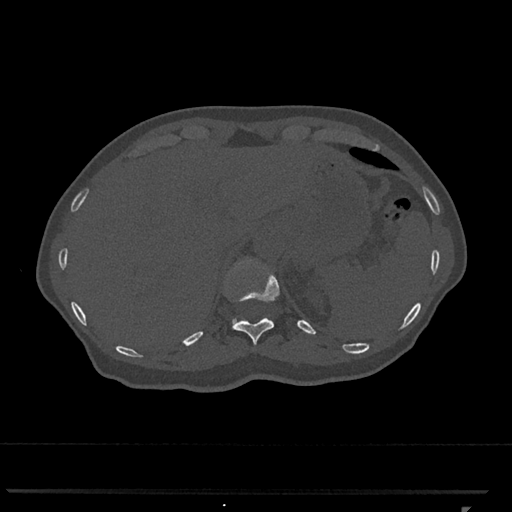
CT including the spine, one axial slice; reconstruction kernel Br40s/3; 120 kVp; bone window (W 1800 / L 400 HU); 0.5 mm slice thickness; 512 × 512 image matrix, field of view 380 × 380 mm. Patient: female, 62 years. Case-level facts recorded for this patient, not image findings: primary cancer: renal.
Outlined on this slice (semi-automatically segmented with operator editing):
- T11 vertebra: bounding box [x1, y1, x2, y2] px = [232, 260, 280, 346]
- T12 vertebra: [232, 318, 241, 324]